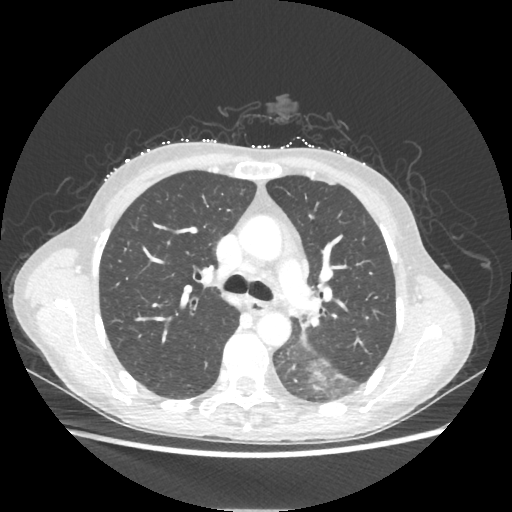
Chest CT, one axial slice. Slice 139 of 221 in the series (ordered by position). 80 kVp. Lung window (W 1500 / L -600 HU). 1.25 mm slice thickness. 512 × 512 image matrix, field of view 360 × 360 mm. Patient: female, 53 years. From the clinical record (not read from this slice): clinical TNM (as recorded): T3 N0 M0.
Outlined on this slice (bounding box drawn by a radiologist):
- lung tumour (recorded histology: adenocarcinoma): bounding box [x1, y1, x2, y2] px = [314, 371, 344, 390]